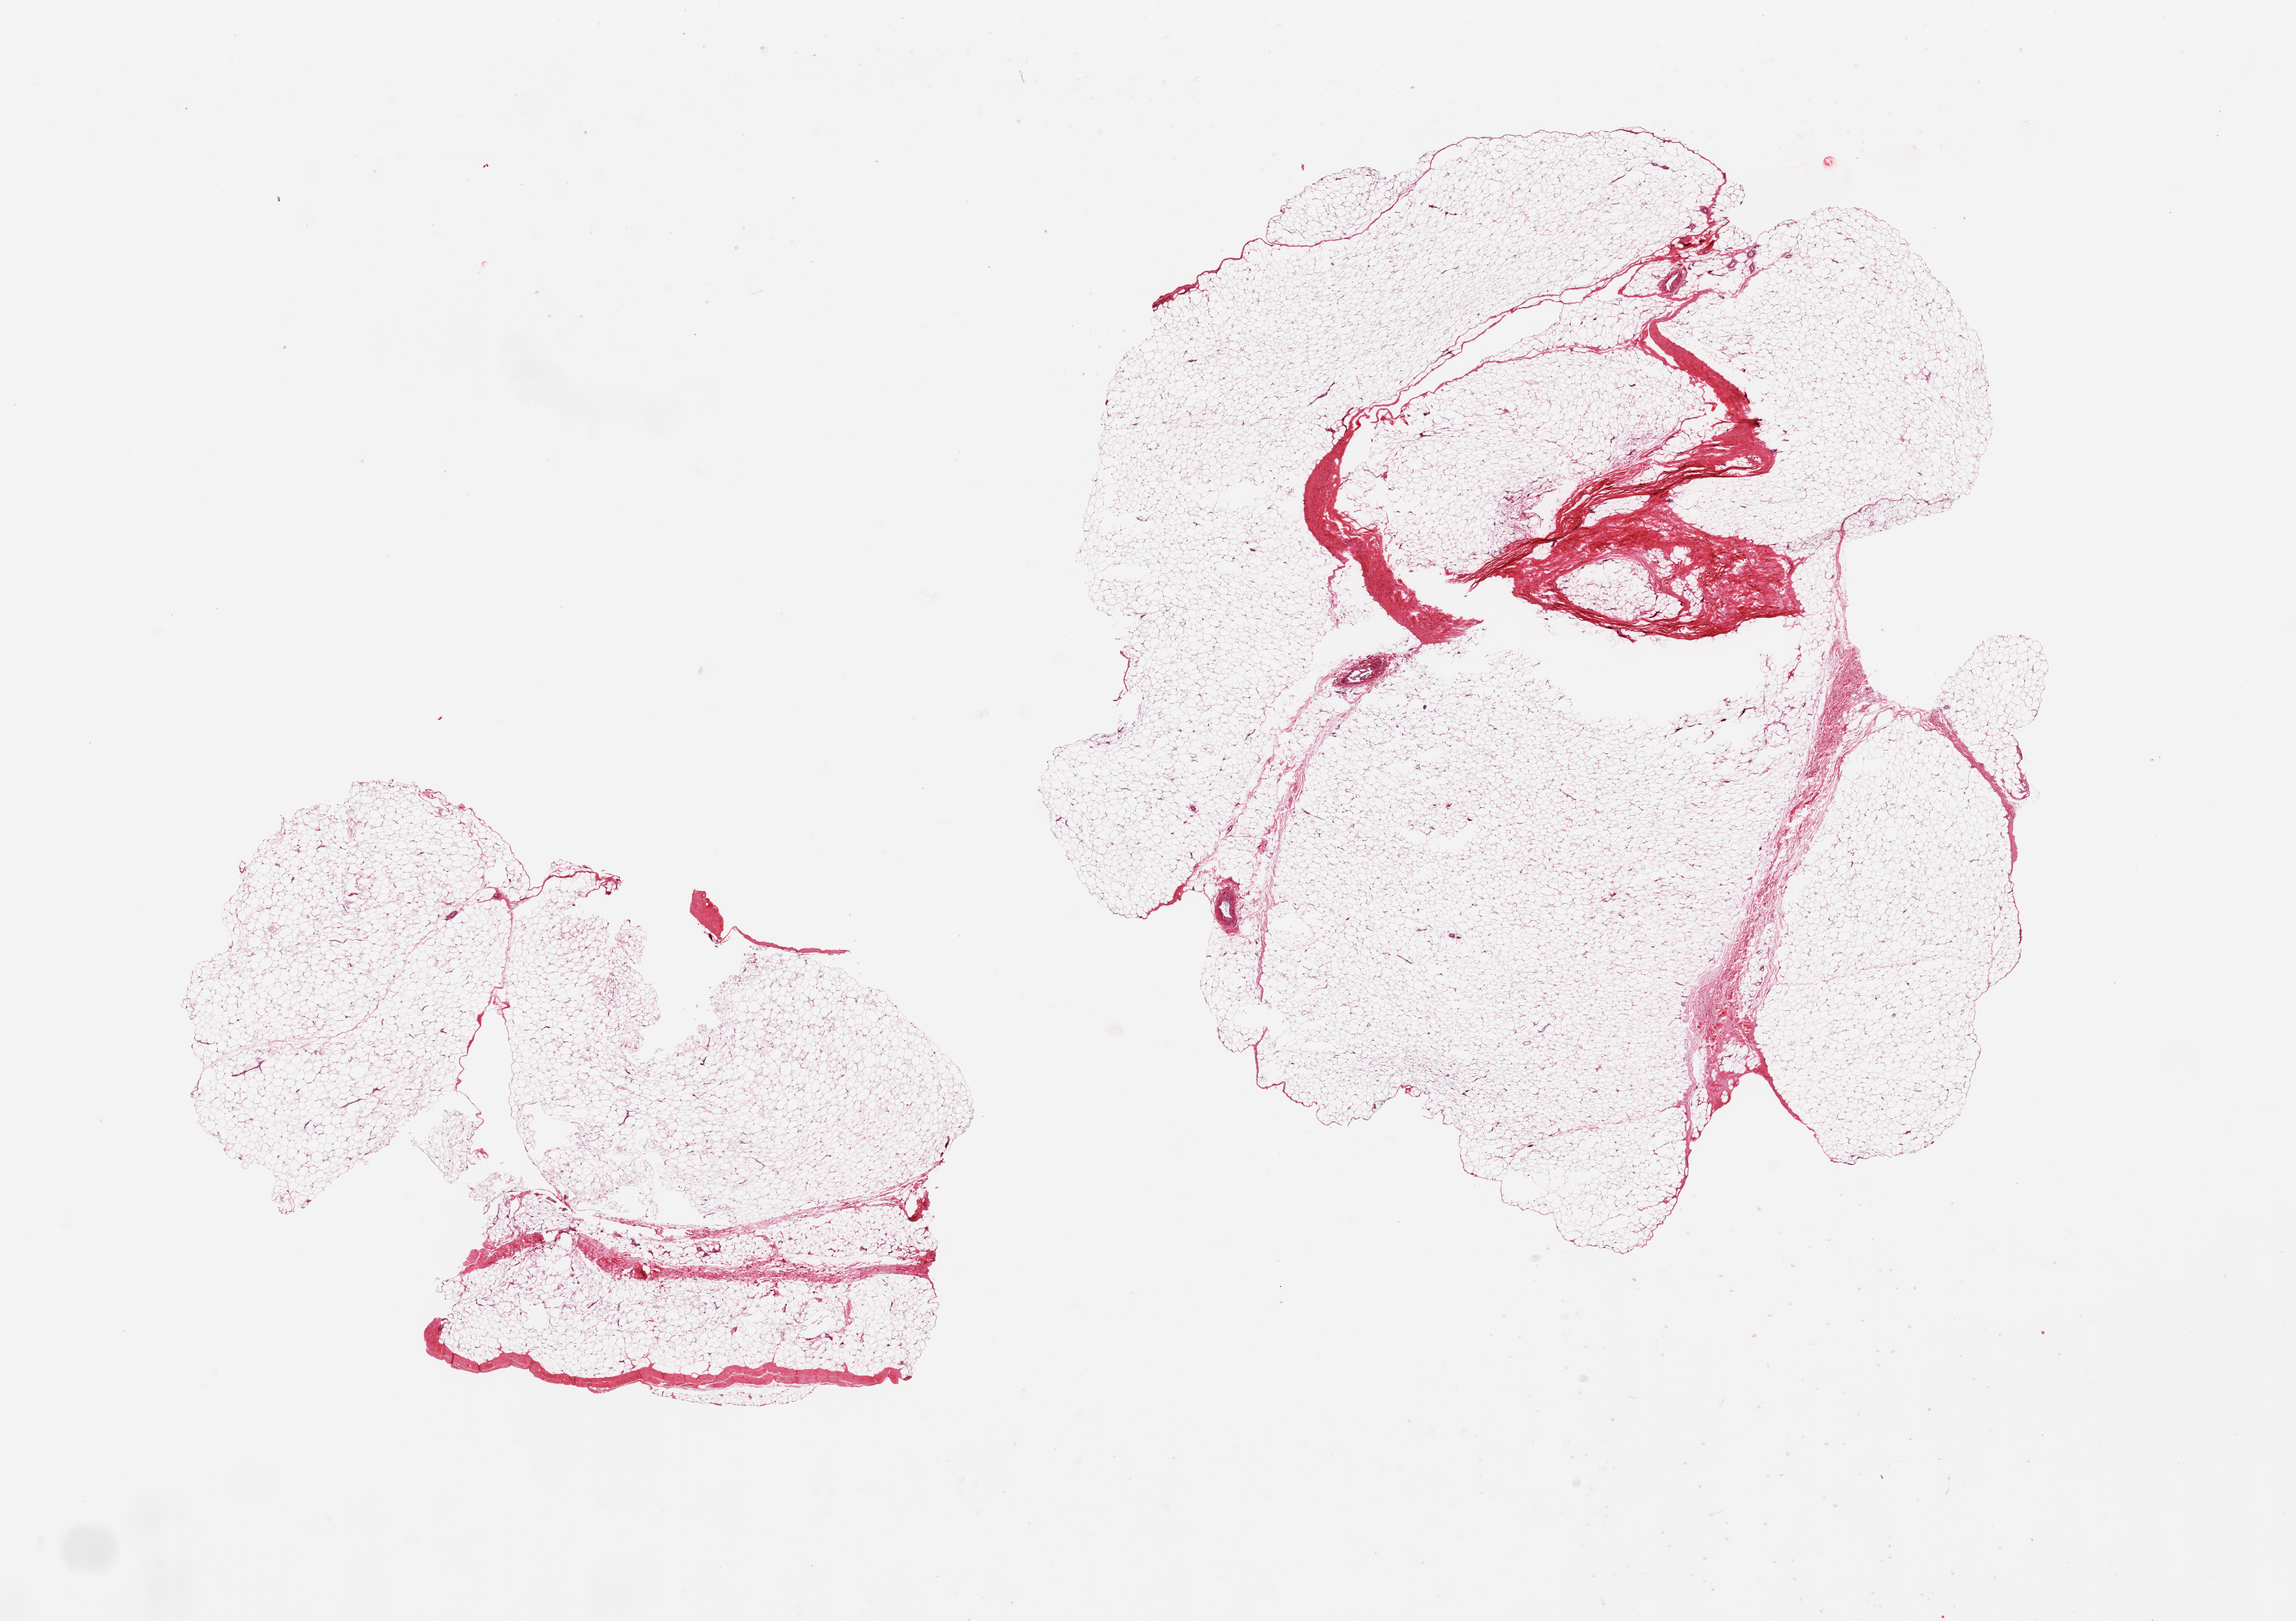
Digitized haematoxylin and eosin-stained section — whole scanned area (about 25.6 x 18.1 mm, slide scanned at 20x) shown as a low-resolution overview; PAXgene-fixed, paraffin-embedded tissue; sampled site (target tissue): adipose tissue; donor tissue sample. Female donor.
Pathologist's review note for this sample: 2 pieces; adipose tissue with ~5-10% fibrous tissue.